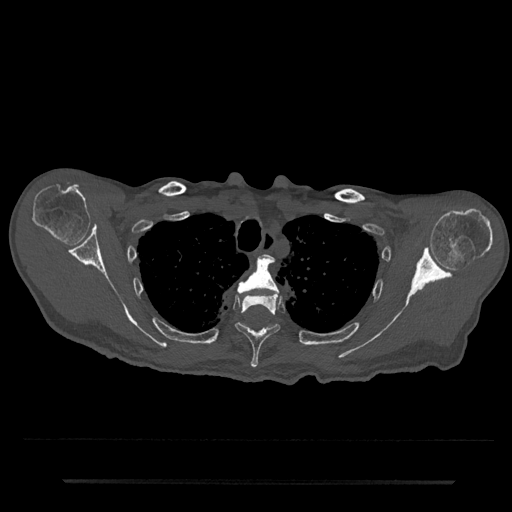
CT including the spine, one axial slice; position 624 of 797 along the scan axis; reconstruction kernel Br40s/3; 120 kVp; bone window (W 1800 / L 400 HU); 0.5 mm slice thickness; 512 × 512 image matrix, field of view 427 × 427 mm. Male patient, age 74 years. Case-level facts recorded for this patient, not image findings: primary cancer: prostate.
Outlined on this slice (semi-automatic segmentation, software-assisted and operator-edited):
- T2 vertebra: box from (x=265, y=256) to (x=268, y=259) px
- T3 vertebra: (x=237, y=256)–(x=279, y=295)
- T4 vertebra: (x=234, y=293)–(x=280, y=368)
- T5 vertebra: (x=260, y=328)–(x=266, y=332)